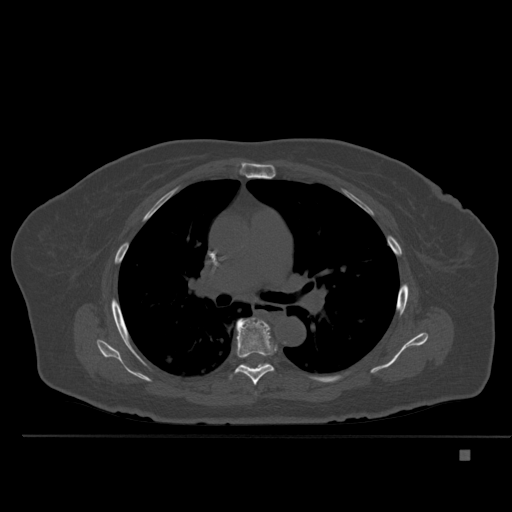
CT including the spine, one axial slice. Slice 338 of 477 in the series (ordered by position). Bone window (W 1800 / L 400 HU). 512 × 512 image matrix. Female patient, age 74 years. From the clinical record (not read from this slice): primary cancer: colon.
Annotated regions visible in this slice (semi-automatically segmented with operator editing):
- T6 vertebra: bounding box [x1, y1, x2, y2] px = [235, 317, 274, 385]
- T7 vertebra: [258, 363, 267, 368]